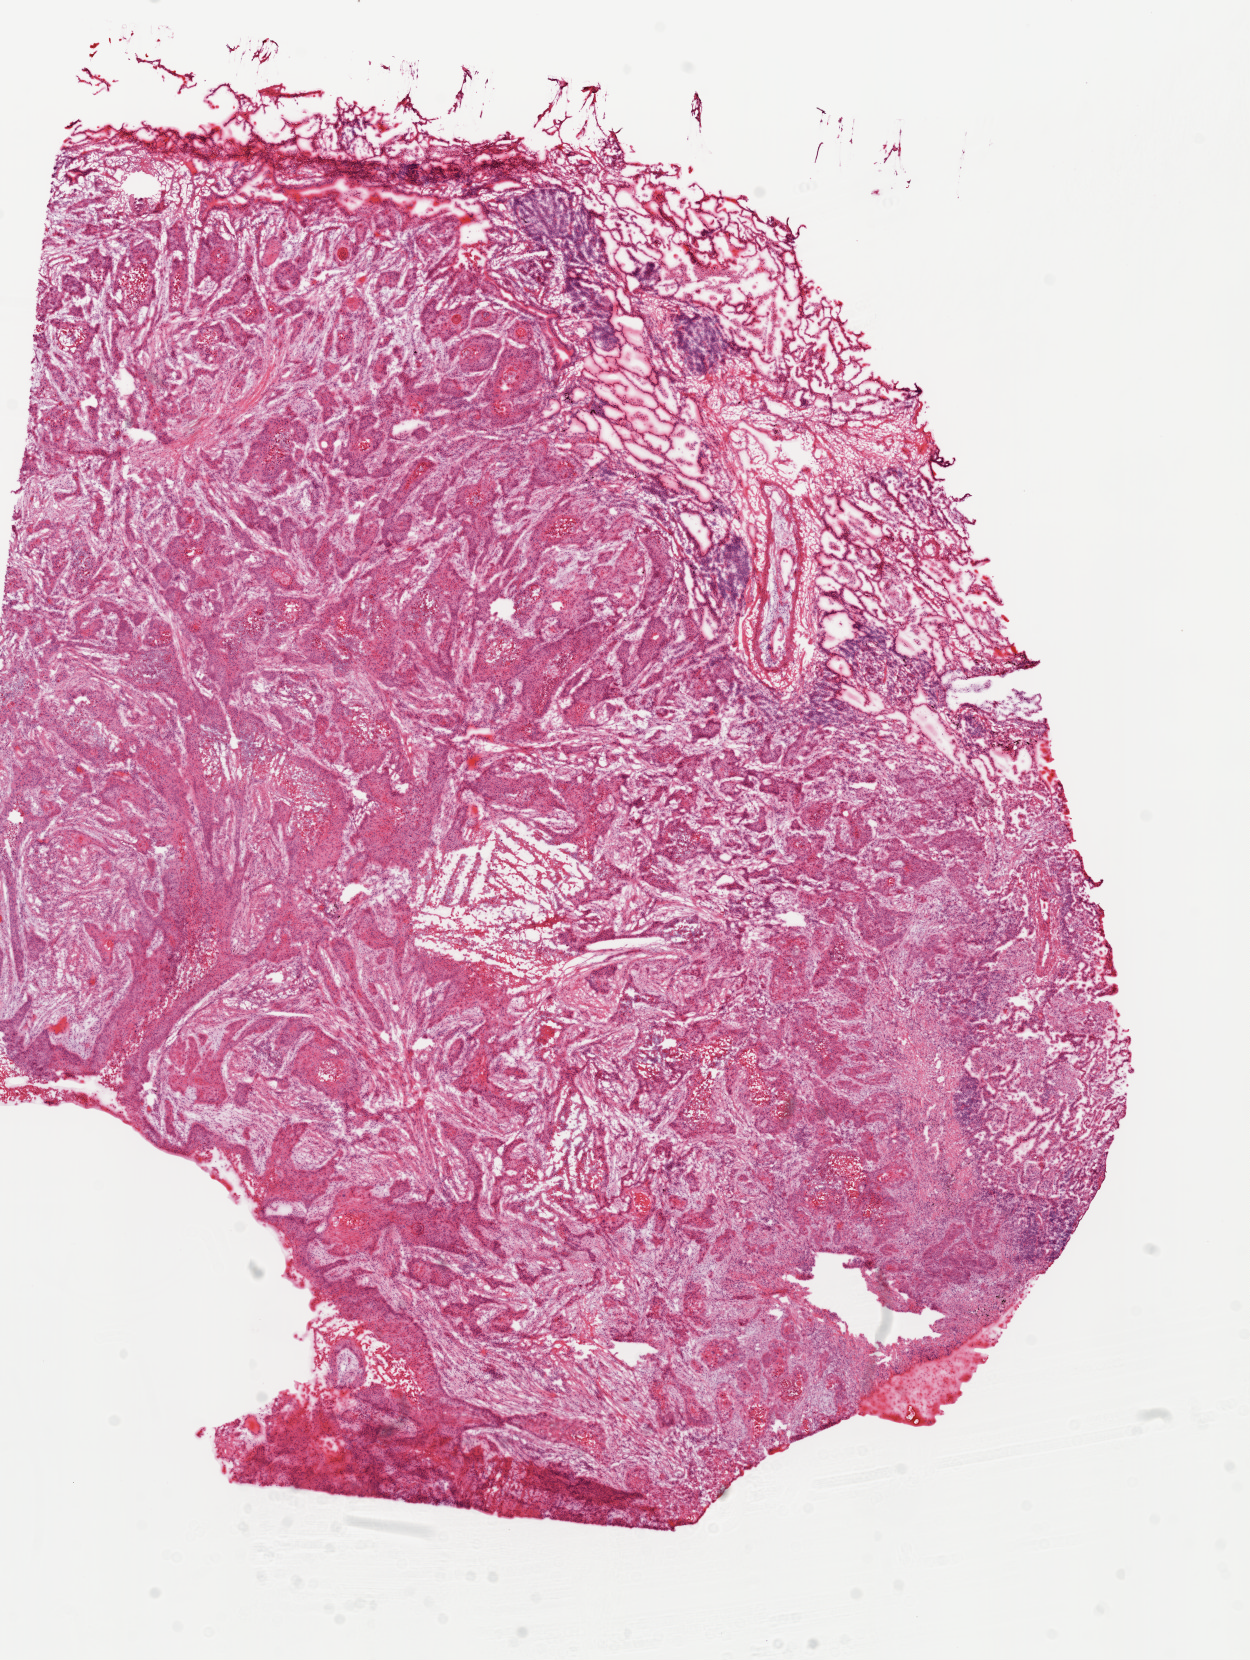
Whole-slide histology image, H&E-stained — whole scanned area (about 10.0 x 13.3 mm) shown as a low-resolution overview. Frozen section. Lung, primary tumour sample. Male patient; age at initial diagnosis 81 years. Composition of this section per pathologist review: tumour cells 88%, tumour nuclei 80%, normal cells 0%, stromal cells 6%, necrosis 6%. Inflammatory infiltration, as recorded: lymphocyte infiltration 4%, monocyte infiltration 1%, neutrophil infiltration 2%.
Histologic diagnosis: Squamous cell carcinoma, NOS (upper lobe, lung). TNM: T2a N0 M0. AJCC pathologic stage: IB.